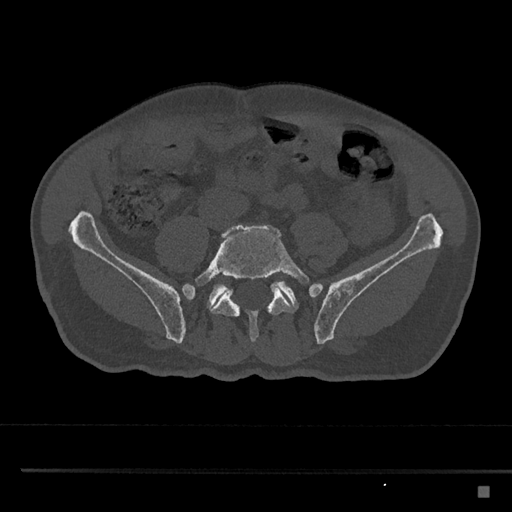
CT including the spine, one axial slice; slice 573 of 797 in the series (ordered by position); reconstruction kernel Br40s/3; bone window (W 1800 / L 400 HU); 512 × 512 image matrix, field of view 391 × 391 mm. Male patient, age 59 years. Case-level facts recorded for this patient, not image findings: primary cancer: prostate.
Structures marked on this image (semi-automatic segmentation, software-assisted and operator-edited):
- L5 vertebra: bounding box (x1, y1, x2, y2) in pixels: (182, 224, 309, 342)